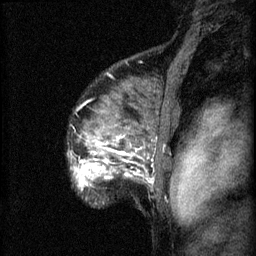
Breast MRI (dynamic contrast-enhanced), one sagittal slice. Slice 51 of 60 in the series (ordered by position). 3 images stored at this slice position (order not interpretable as contrast timing). 1.5 T. TE 4.2 ms, TR 8.2 ms. 2 mm slice thickness. 256 × 256 image matrix. Patient: female, 48 years.
Outlined on this slice (semi-automatic segmentation, software-assisted and operator-edited):
- analysis volume of interest (the breast-tissue region the enhancement analysis was run in; not a lesion): bounding box <73,138,153,191> (left, top, right, bottom; pixels)
- tumour enhancement mask (voxels above the 70 % enhancement threshold inside the analysis volume of interest): <76,160,152,187>